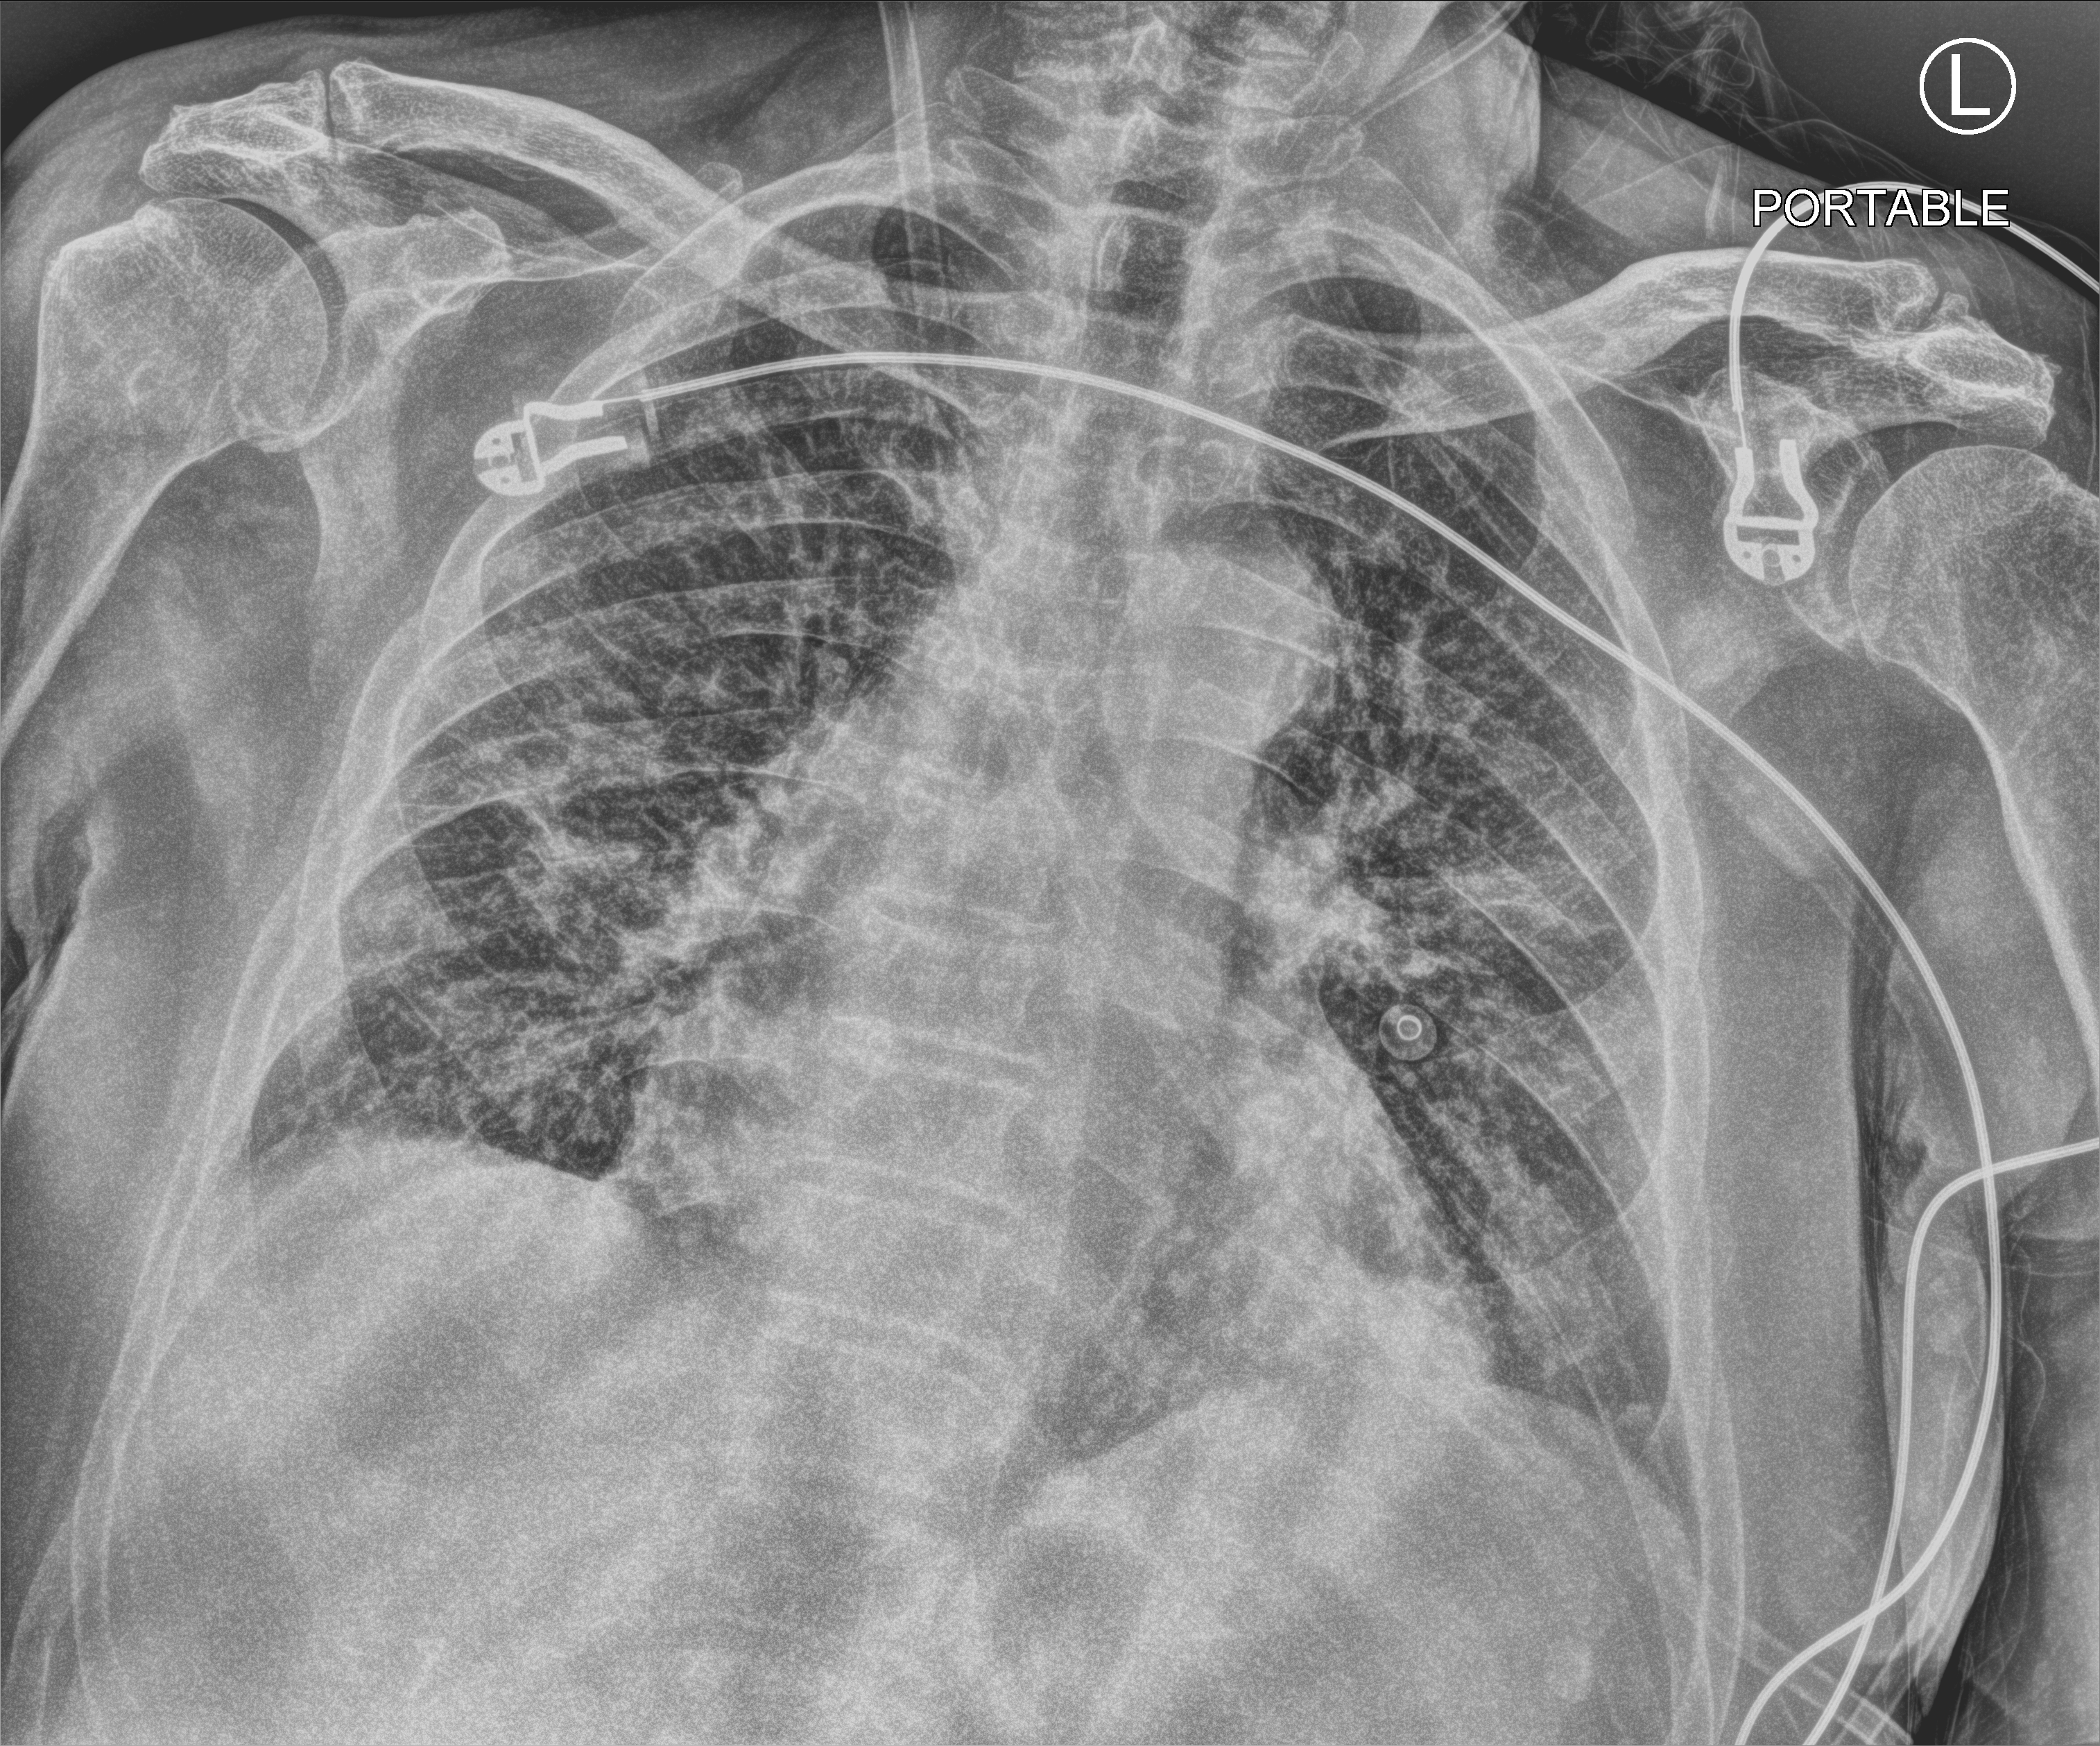
Portable chest radiograph. Male patient hospitalised with COVID-19, age 75–90 years.
Hospital-stay facts (about this admission, not read from this image; timing relative to this image not recorded):
- chronic kidney disease (admission record): no
- admitted to intensive care during this hospital stay: no
- smoking status (admission record): former